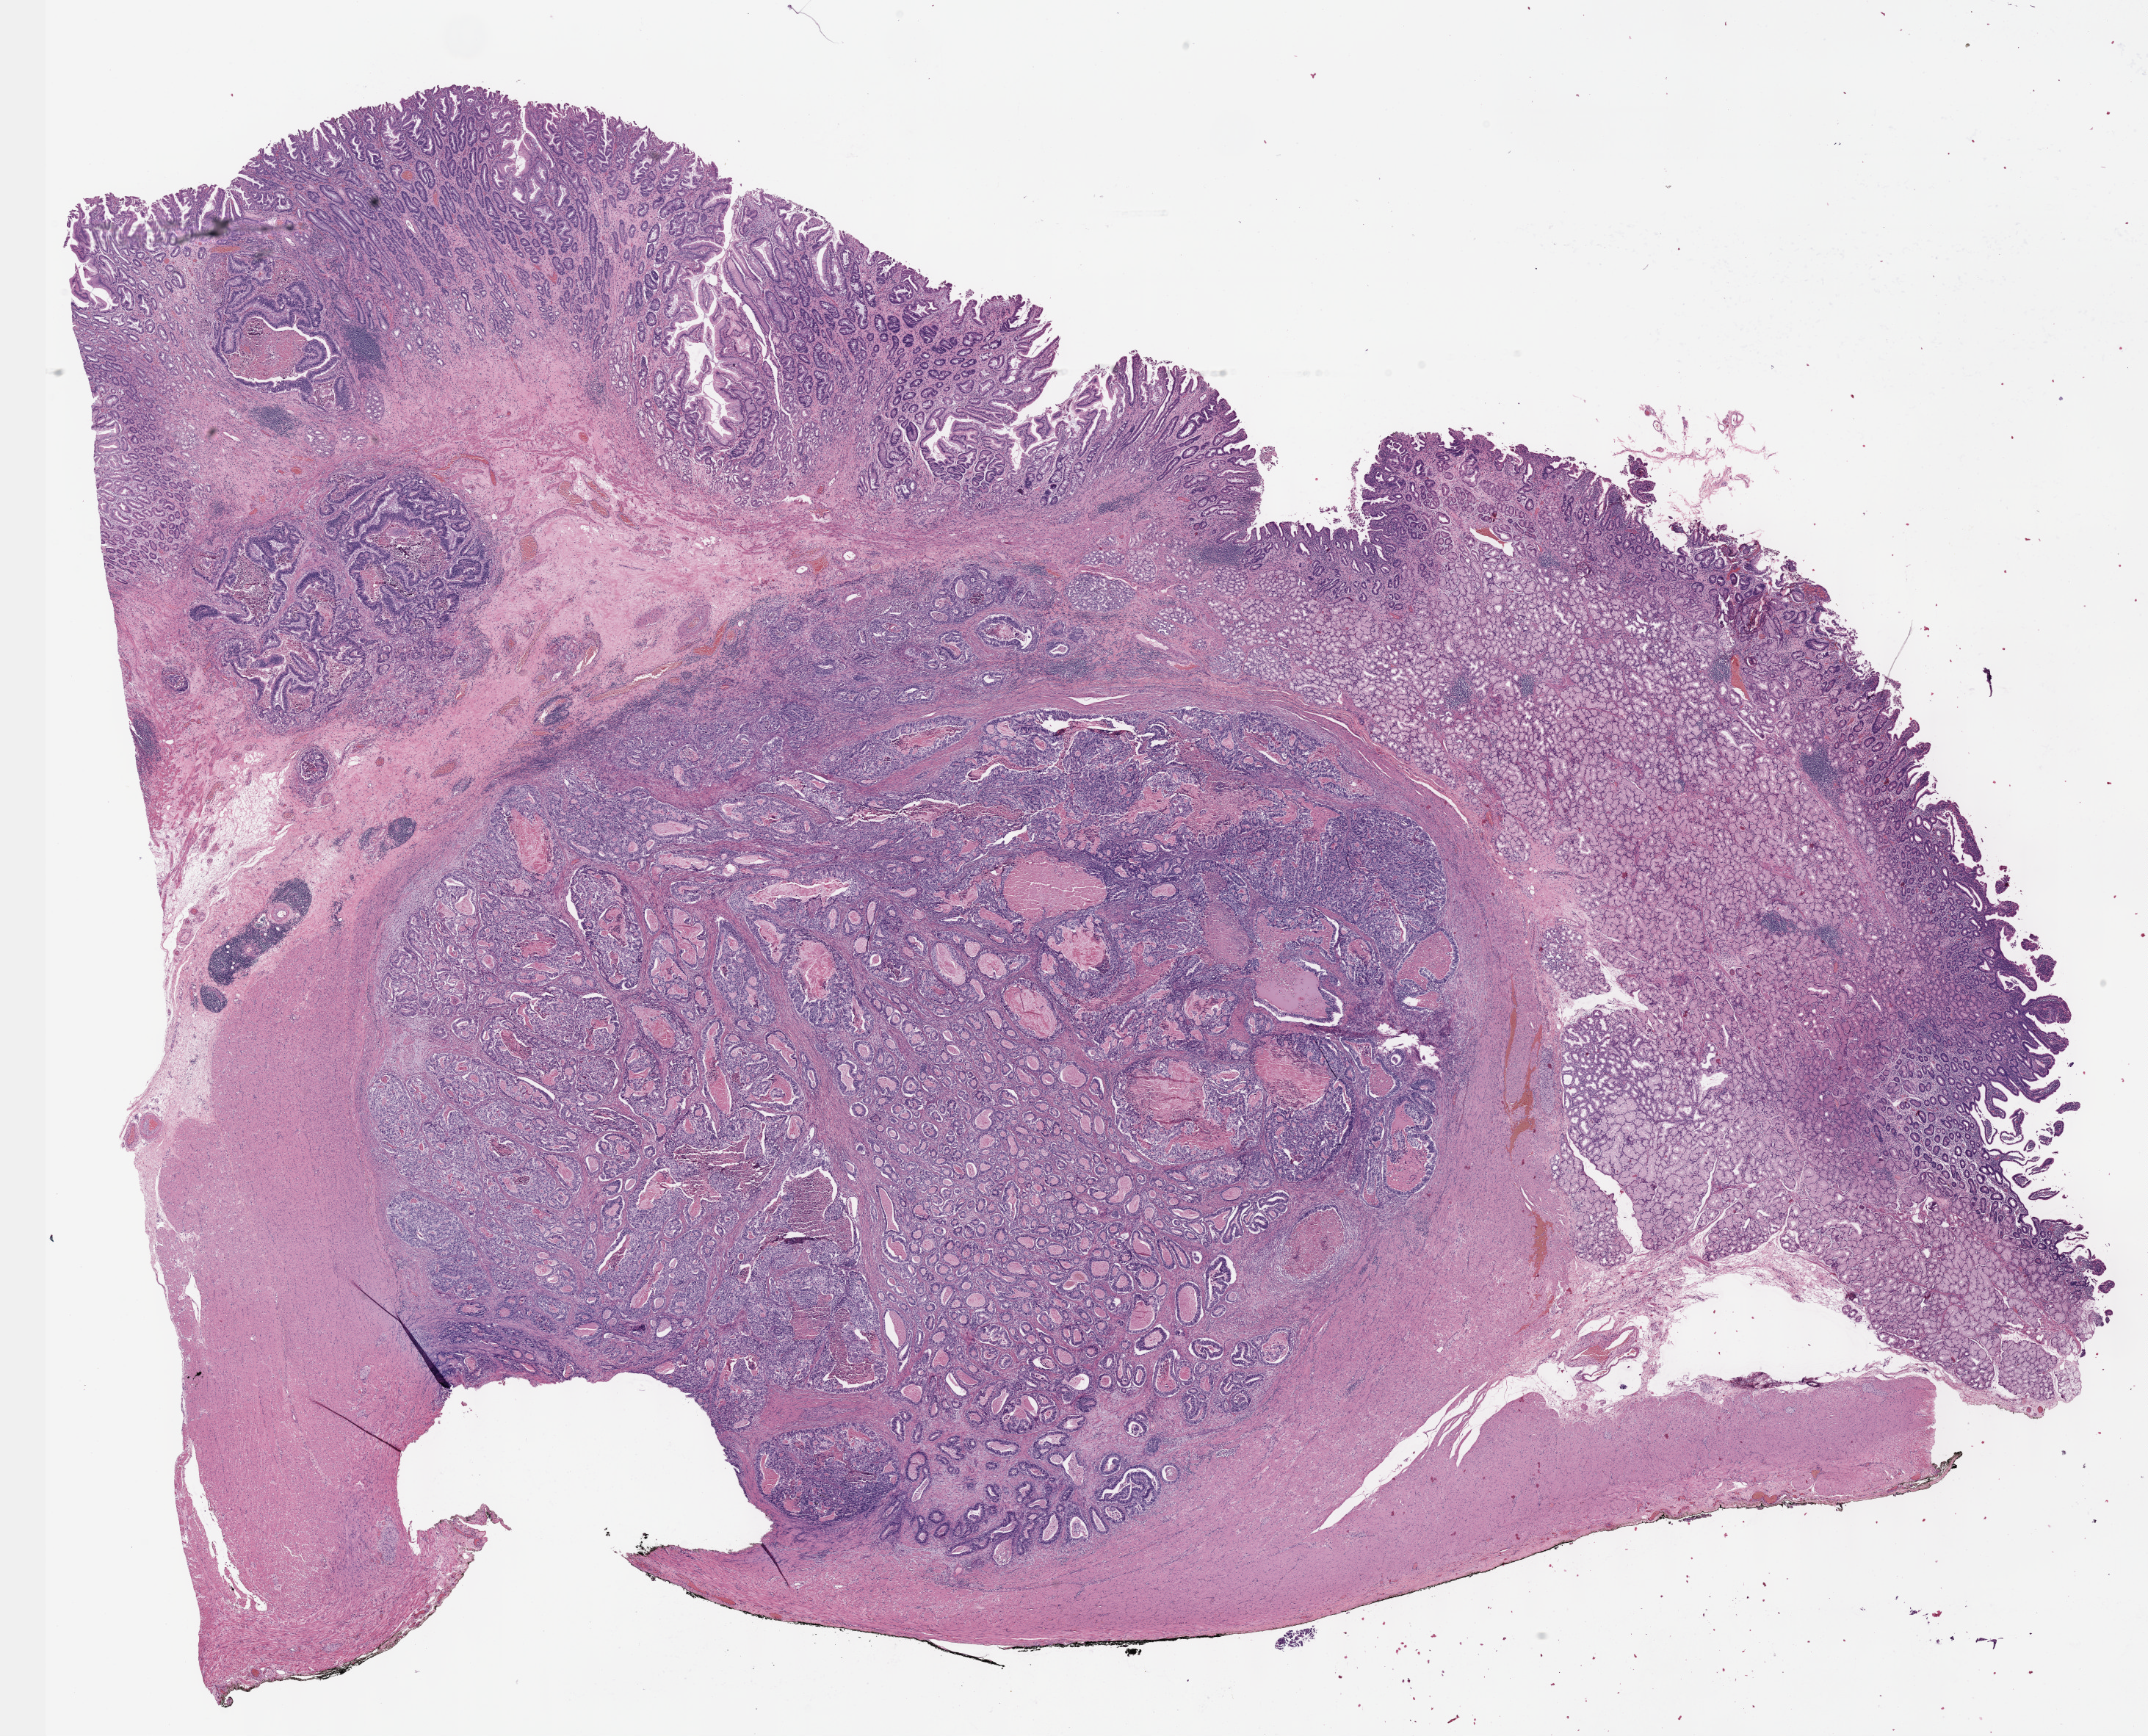
Hematoxylin and eosin (H&E) stained whole-slide image — shown as a low-resolution overview of the whole scanned area (about 23.6 x 19.1 mm, slide scanned at 40x); FFPE section; stomach, primary tumour sample. Male, age 70 years at initial diagnosis. Histologic grade: G2 (moderately differentiated).
* pathologic diagnosis: Tubular adenocarcinoma (gastric antrum)
* AJCC pathologic stage: IV
* lymph nodes positive (case pathology): 1 of 16 examined